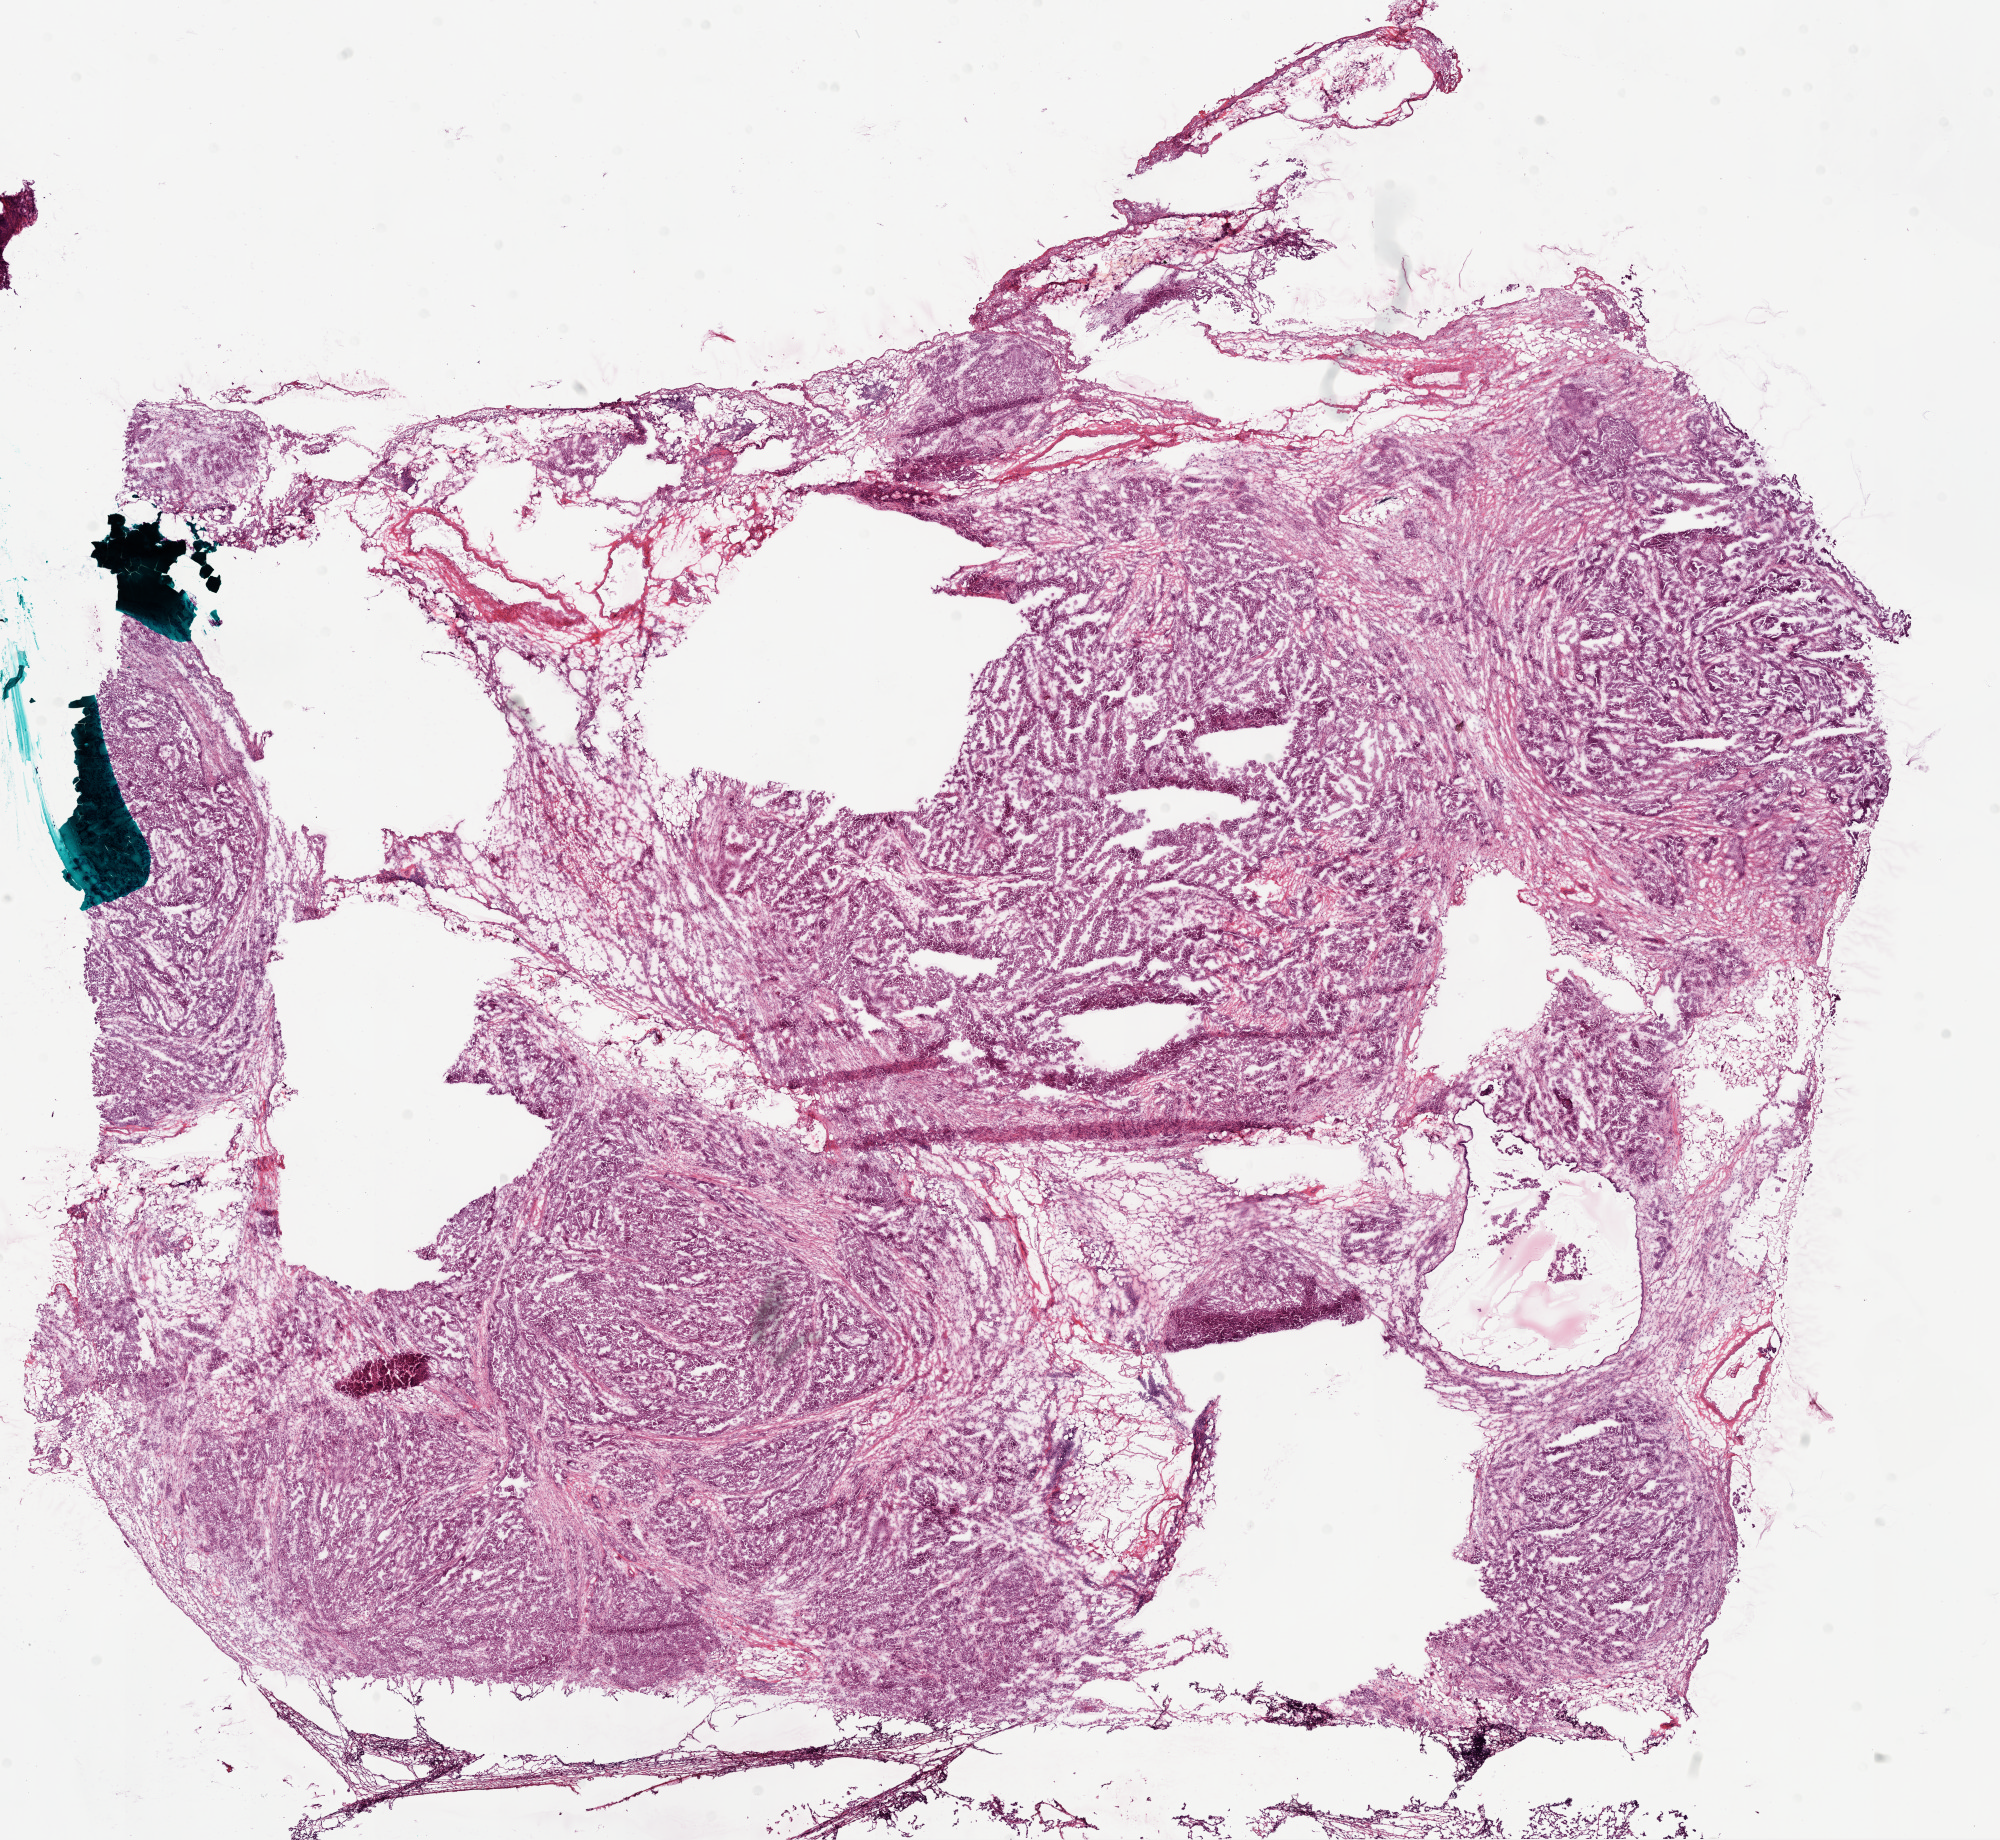
H&E whole-slide image — a low-resolution overview of the entire scanned area, about 16.0 x 14.8 mm, frozen section from the bottom of the tissue portion, ovary, primary tumour sample. Female, age 49 years at initial diagnosis. Histologic grade: G3 (poorly differentiated). Pathologist review of this section (percent, as recorded): tumour cells 84%, tumour nuclei 85%, normal cells 0%, stromal cells 15%, necrosis 1%.
Histologic diagnosis: Serous cystadenocarcinoma, NOS. FIGO stage: IV.